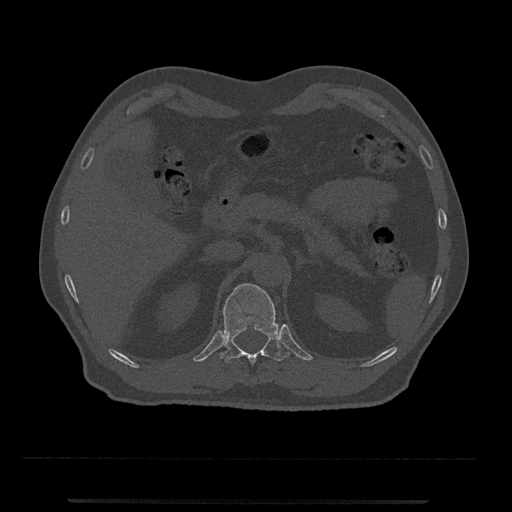
CT including the spine, one axial slice; slice 407 of 797 in the series (ordered by position); bone window (W 1800 / L 400 HU); 0.5 mm slice thickness; 512 × 512 image matrix, field of view 419 × 419 mm. Male patient, age 63 years. Case-level facts recorded for this patient, not image findings: primary cancer: prostate.
Outlined on this slice (semi-automatic segmentation, software-assisted and operator-edited):
- T12 vertebra: bounding box <219,283,290,365> (left, top, right, bottom; pixels)